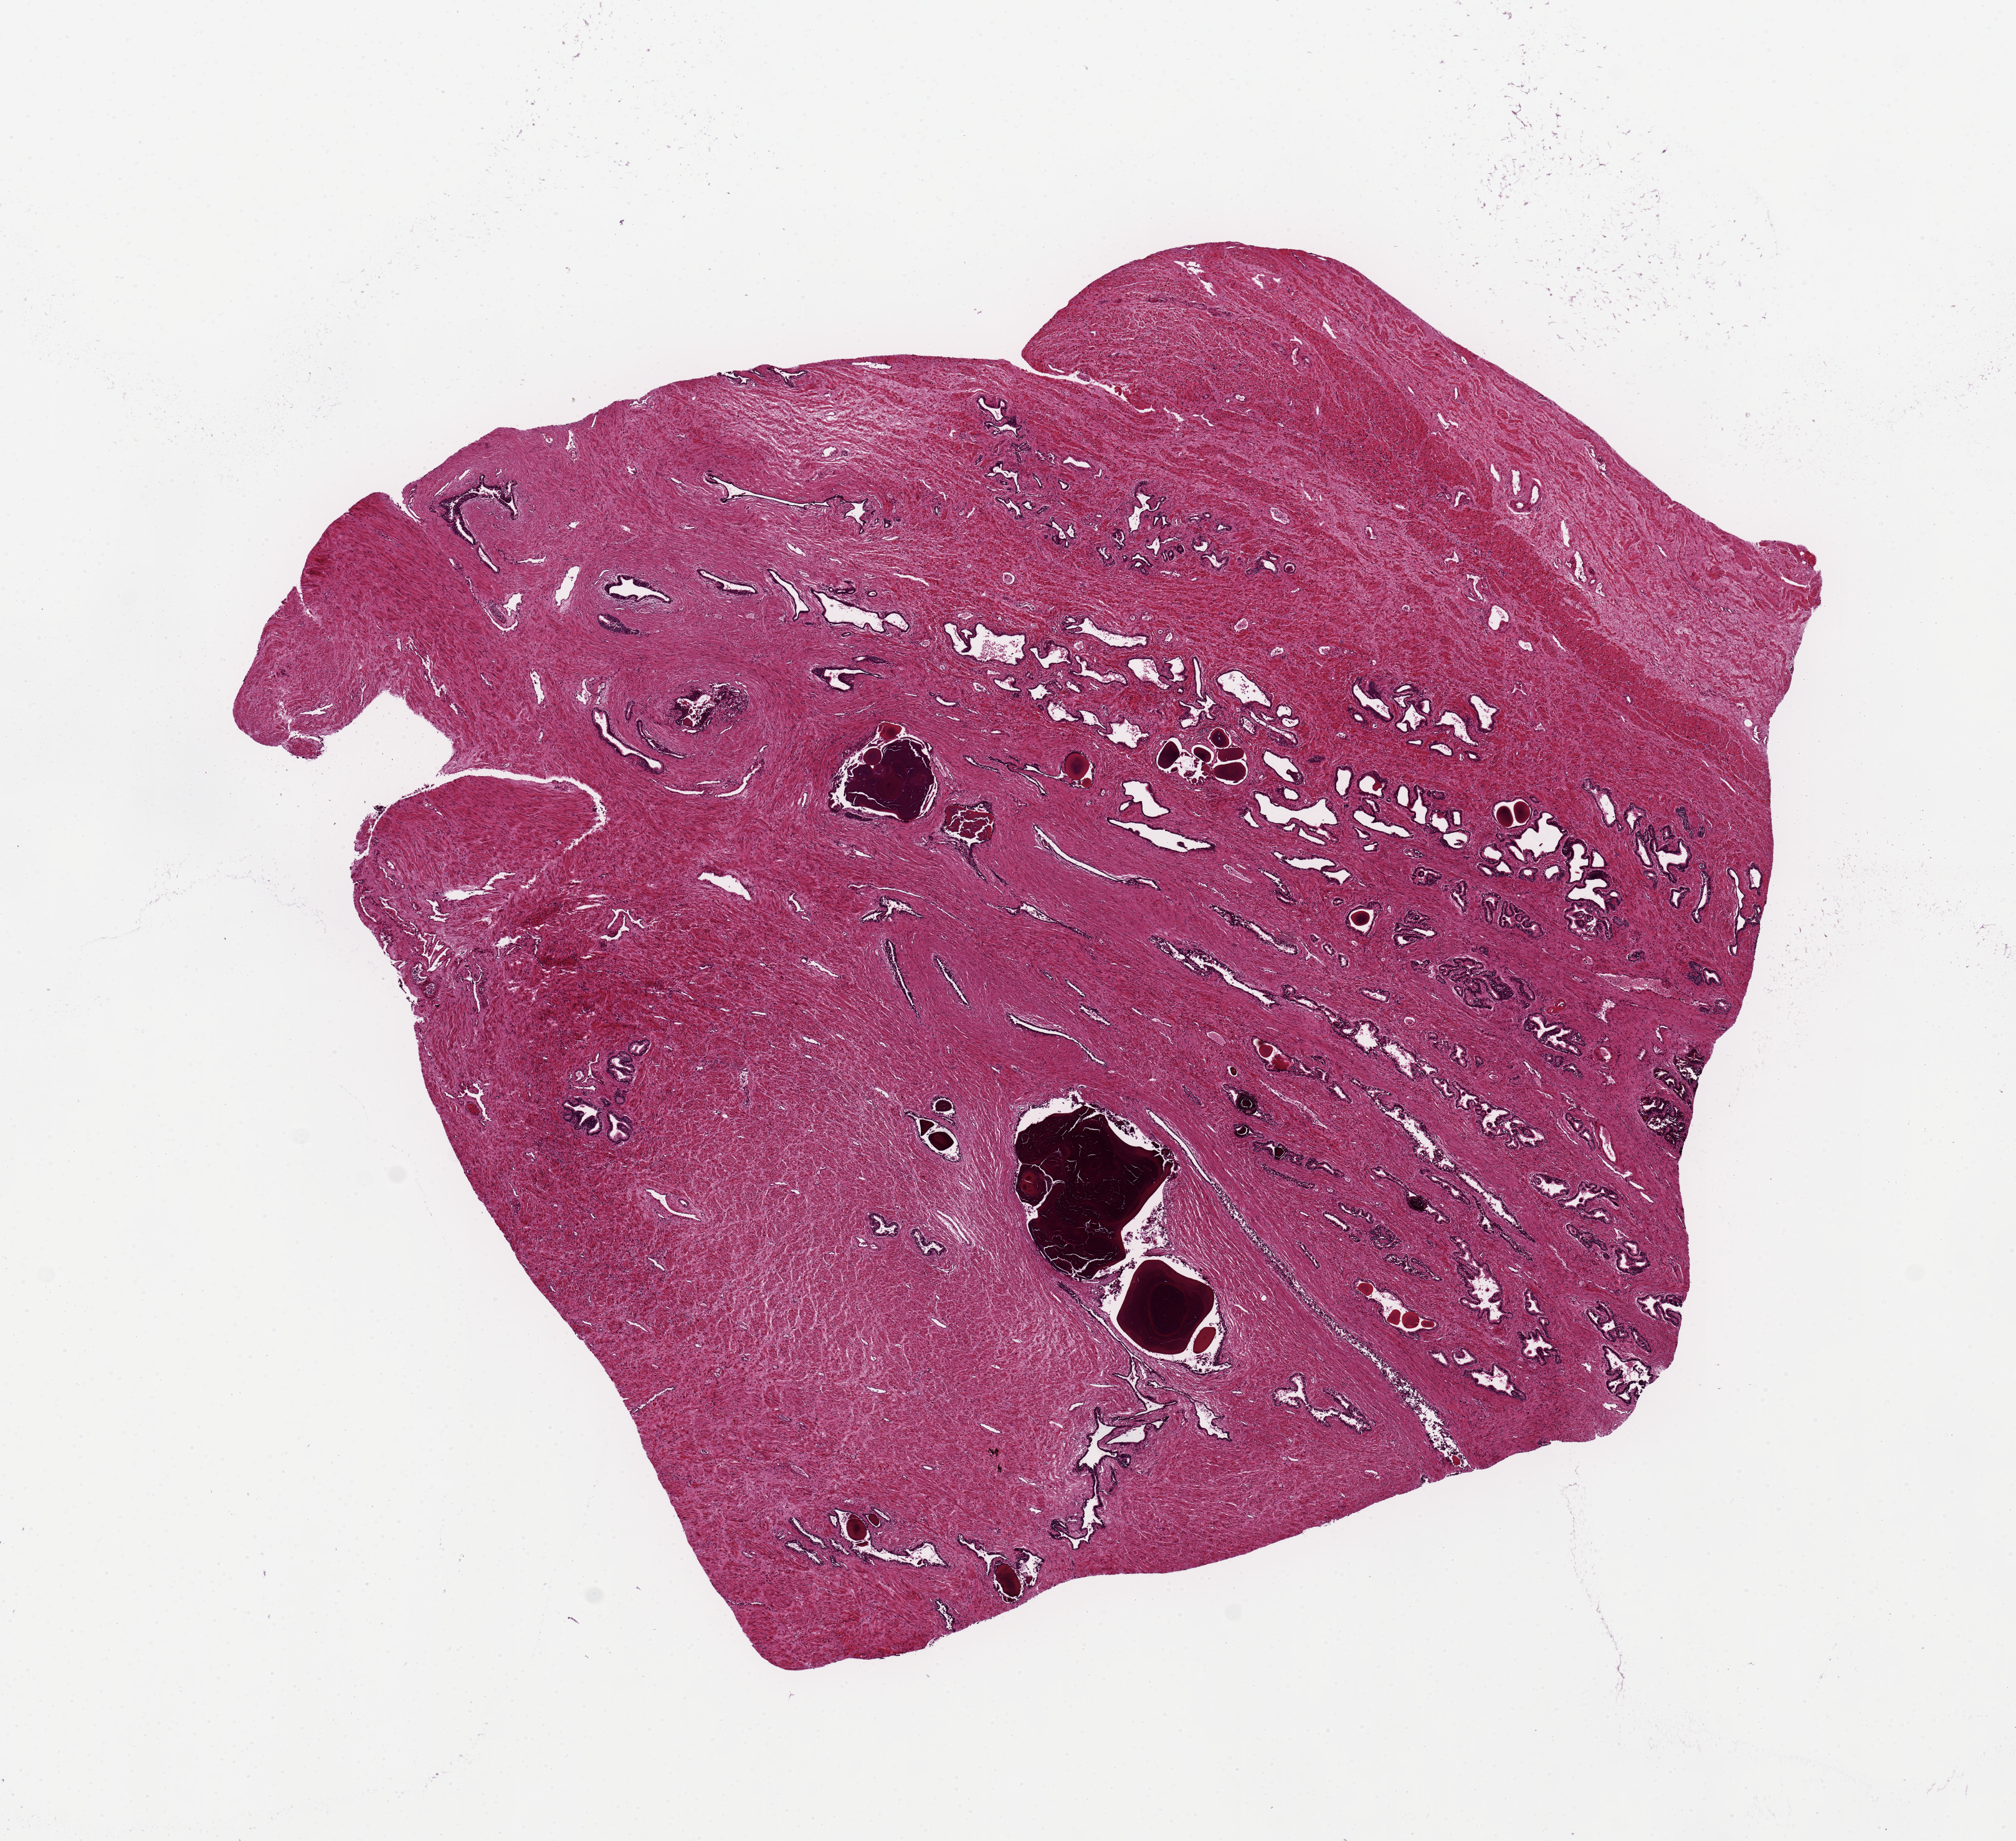
Hematoxylin and eosin (H&E) whole-slide image — whole scanned area (about 12.8 x 11.7 mm, acquisition: 20x scan) shown as a low-resolution overview, PAXgene-fixed, paraffin-embedded tissue, section of prostate (target tissue), tissue donor sample. Donor: male.
Pathologist's review note for this sample: 10x10mm. Moderate glandular atrophy.